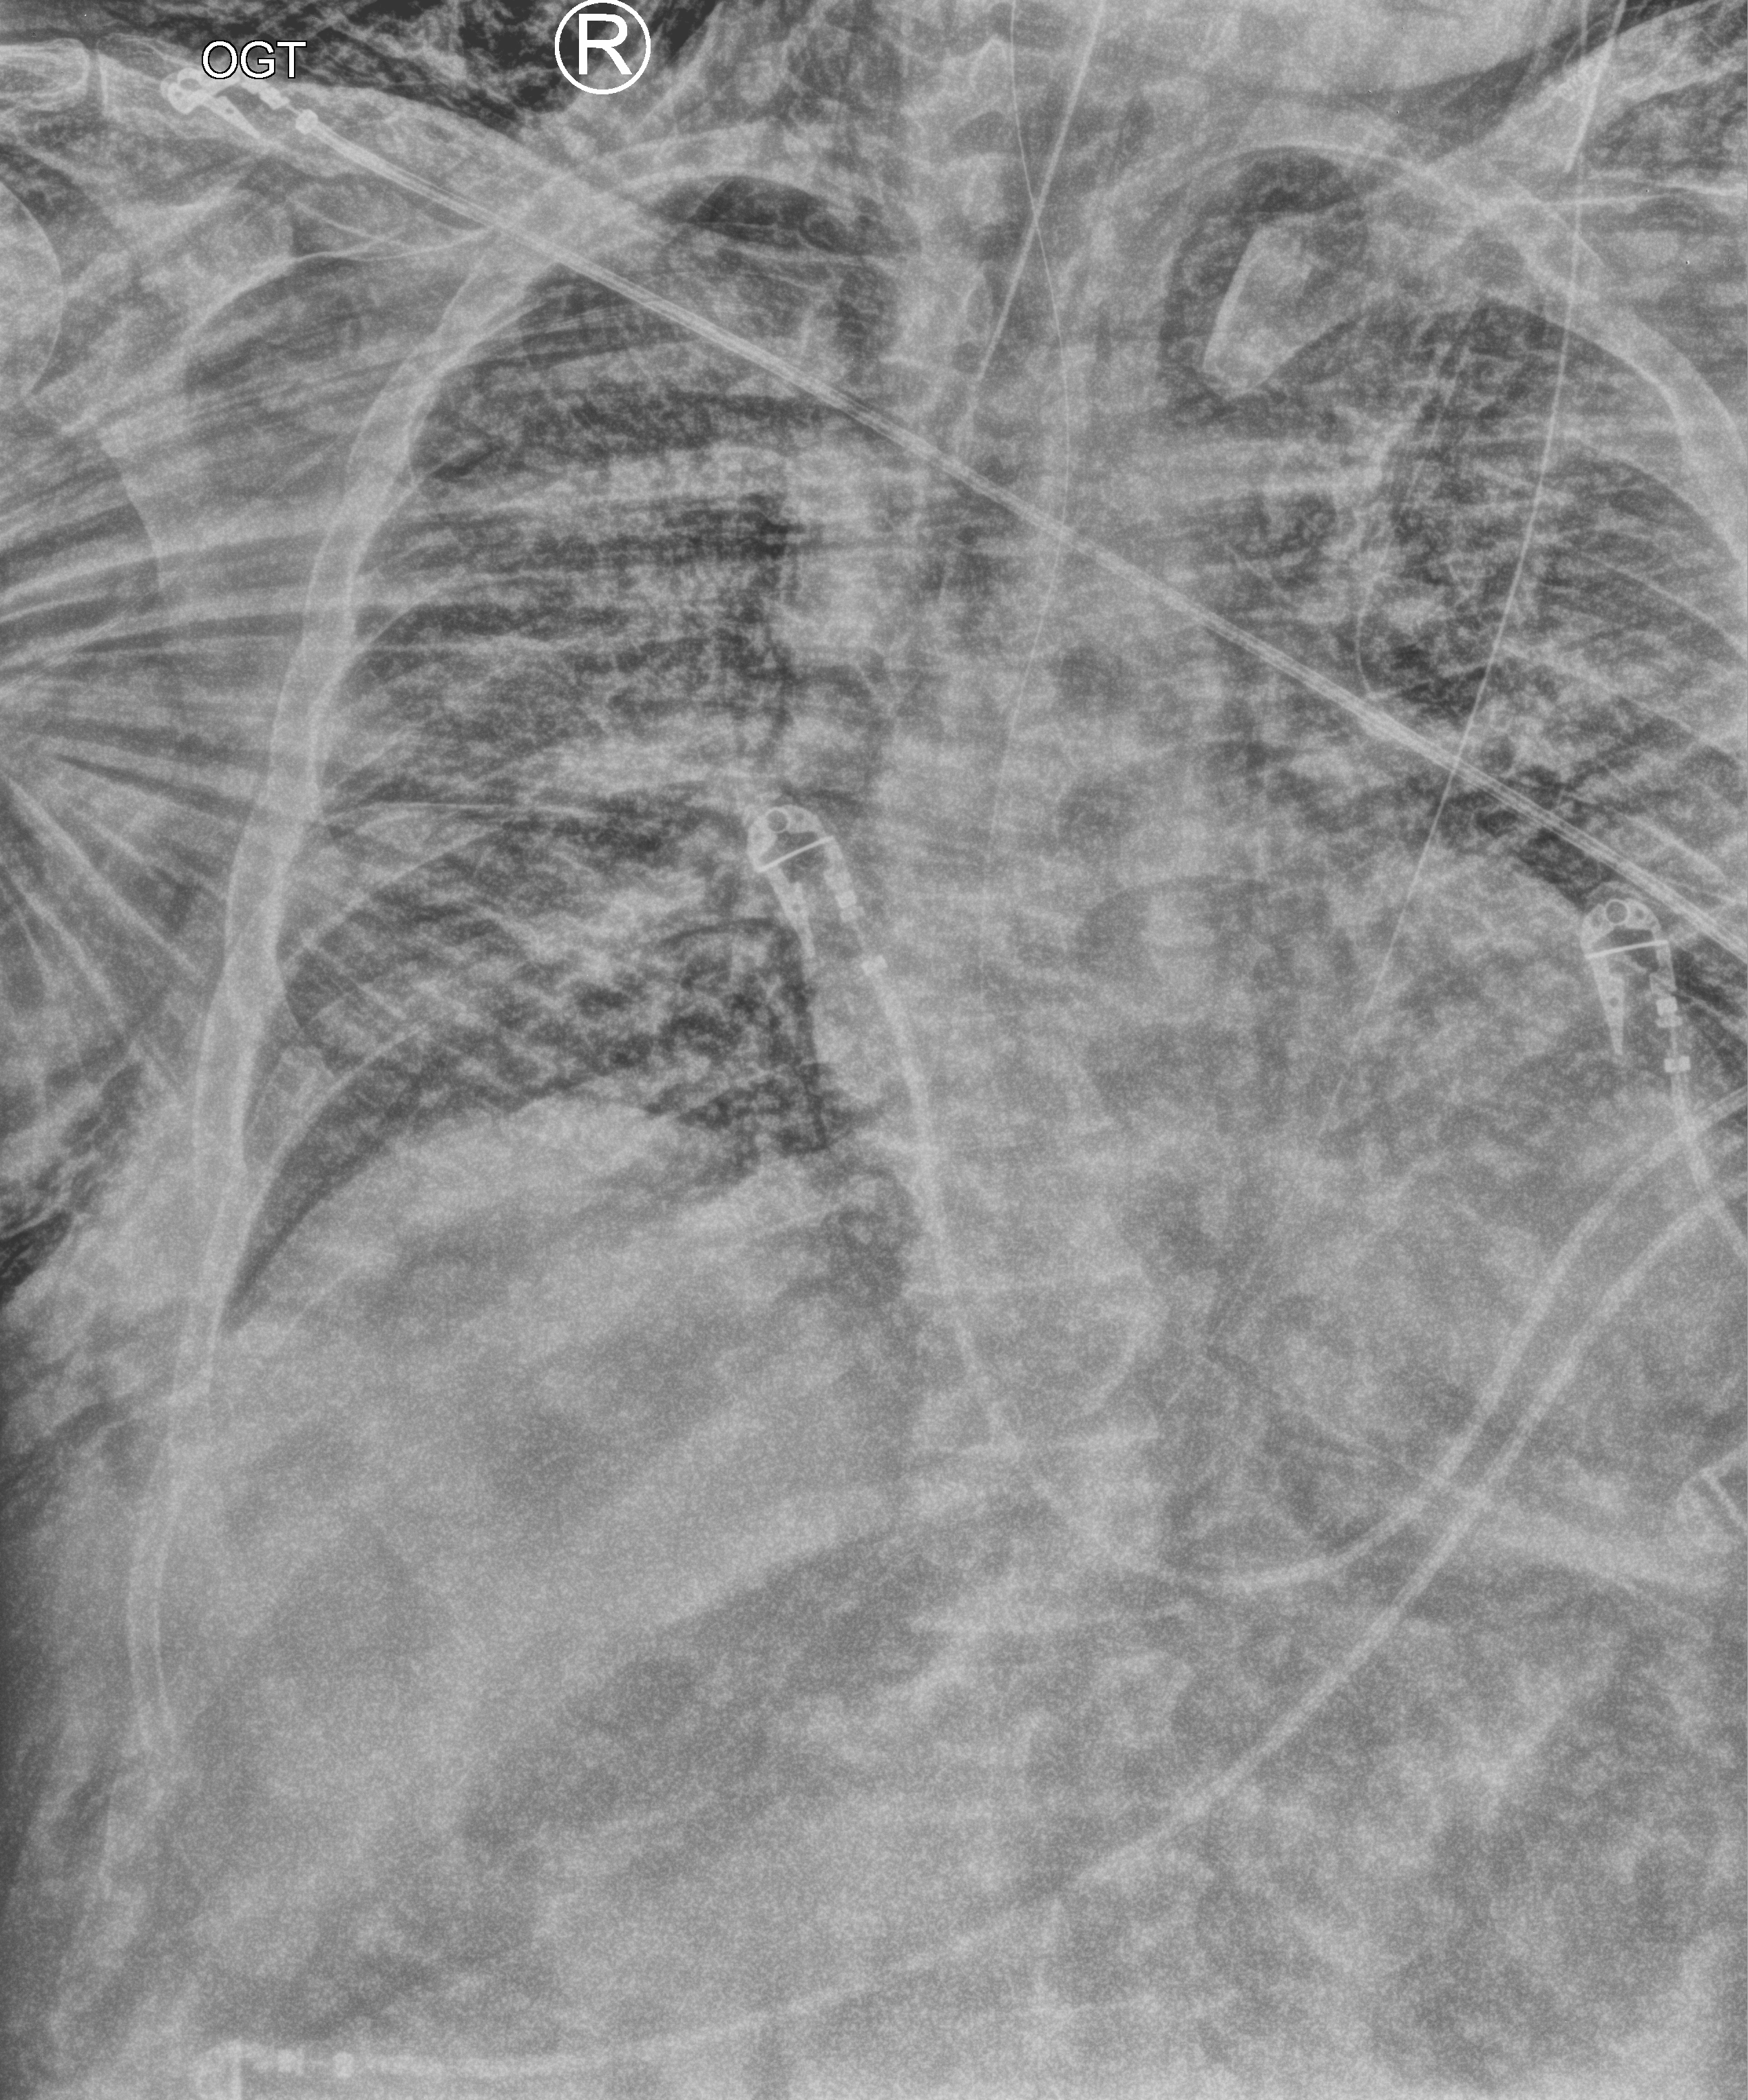
Bedside chest radiograph (computed radiography); anteroposterior (AP) projection. Adult patient hospitalised with COVID-19, age 18–59 years.
Admission-level facts for this patient (not findings on this image; timing relative to this image not recorded): mechanically ventilated during this hospital stay: yes.